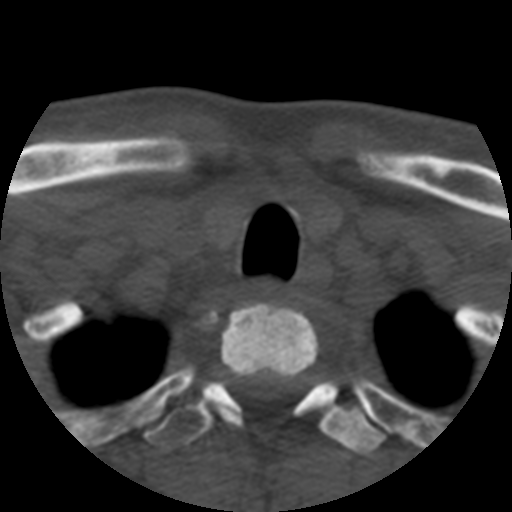
CT including the spine, one axial slice; slice 440 of 508 in the series (ordered by position); reconstruction kernel STANDARD; 120 kVp; bone window (W 1800 / L 400 HU); 1.25 mm slice thickness; 512 × 512 image matrix, field of view 160 × 160 mm. Patient age 57 years. From the clinical record (not read from this slice): primary cancer: prostate.
Annotated regions visible in this slice (semi-automatic segmentation, software-assisted and operator-edited):
- T1 vertebra: box from (x=213, y=303) to (x=319, y=421) px
- T2 vertebra: (x=145, y=374)–(x=384, y=460)